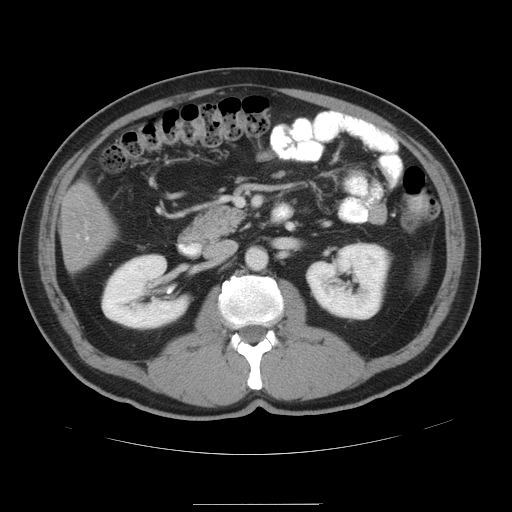
Contrast-enhanced abdominal CT, one axial slice. Slice 19 of 47 in the series (ordered by position). 120 kVp. Intravenous contrast given. Soft-tissue window (W 400 / L 40 HU). 5 mm slice thickness. 512 × 512 image matrix. Male patient, age 61 years. From the clinical record (not read from this slice): diagnosis: colorectal cancer liver metastases, imaged before liver resection; multiple liver metastases: no; largest metastasis: 1.2 cm.
Annotated regions visible in this slice (outlined manually by an expert reader):
- liver: bounding box [x1, y1, x2, y2] px = [62, 183, 115, 270]
- planned liver remnant (the part of the liver to remain after resection): [65, 183, 116, 242]